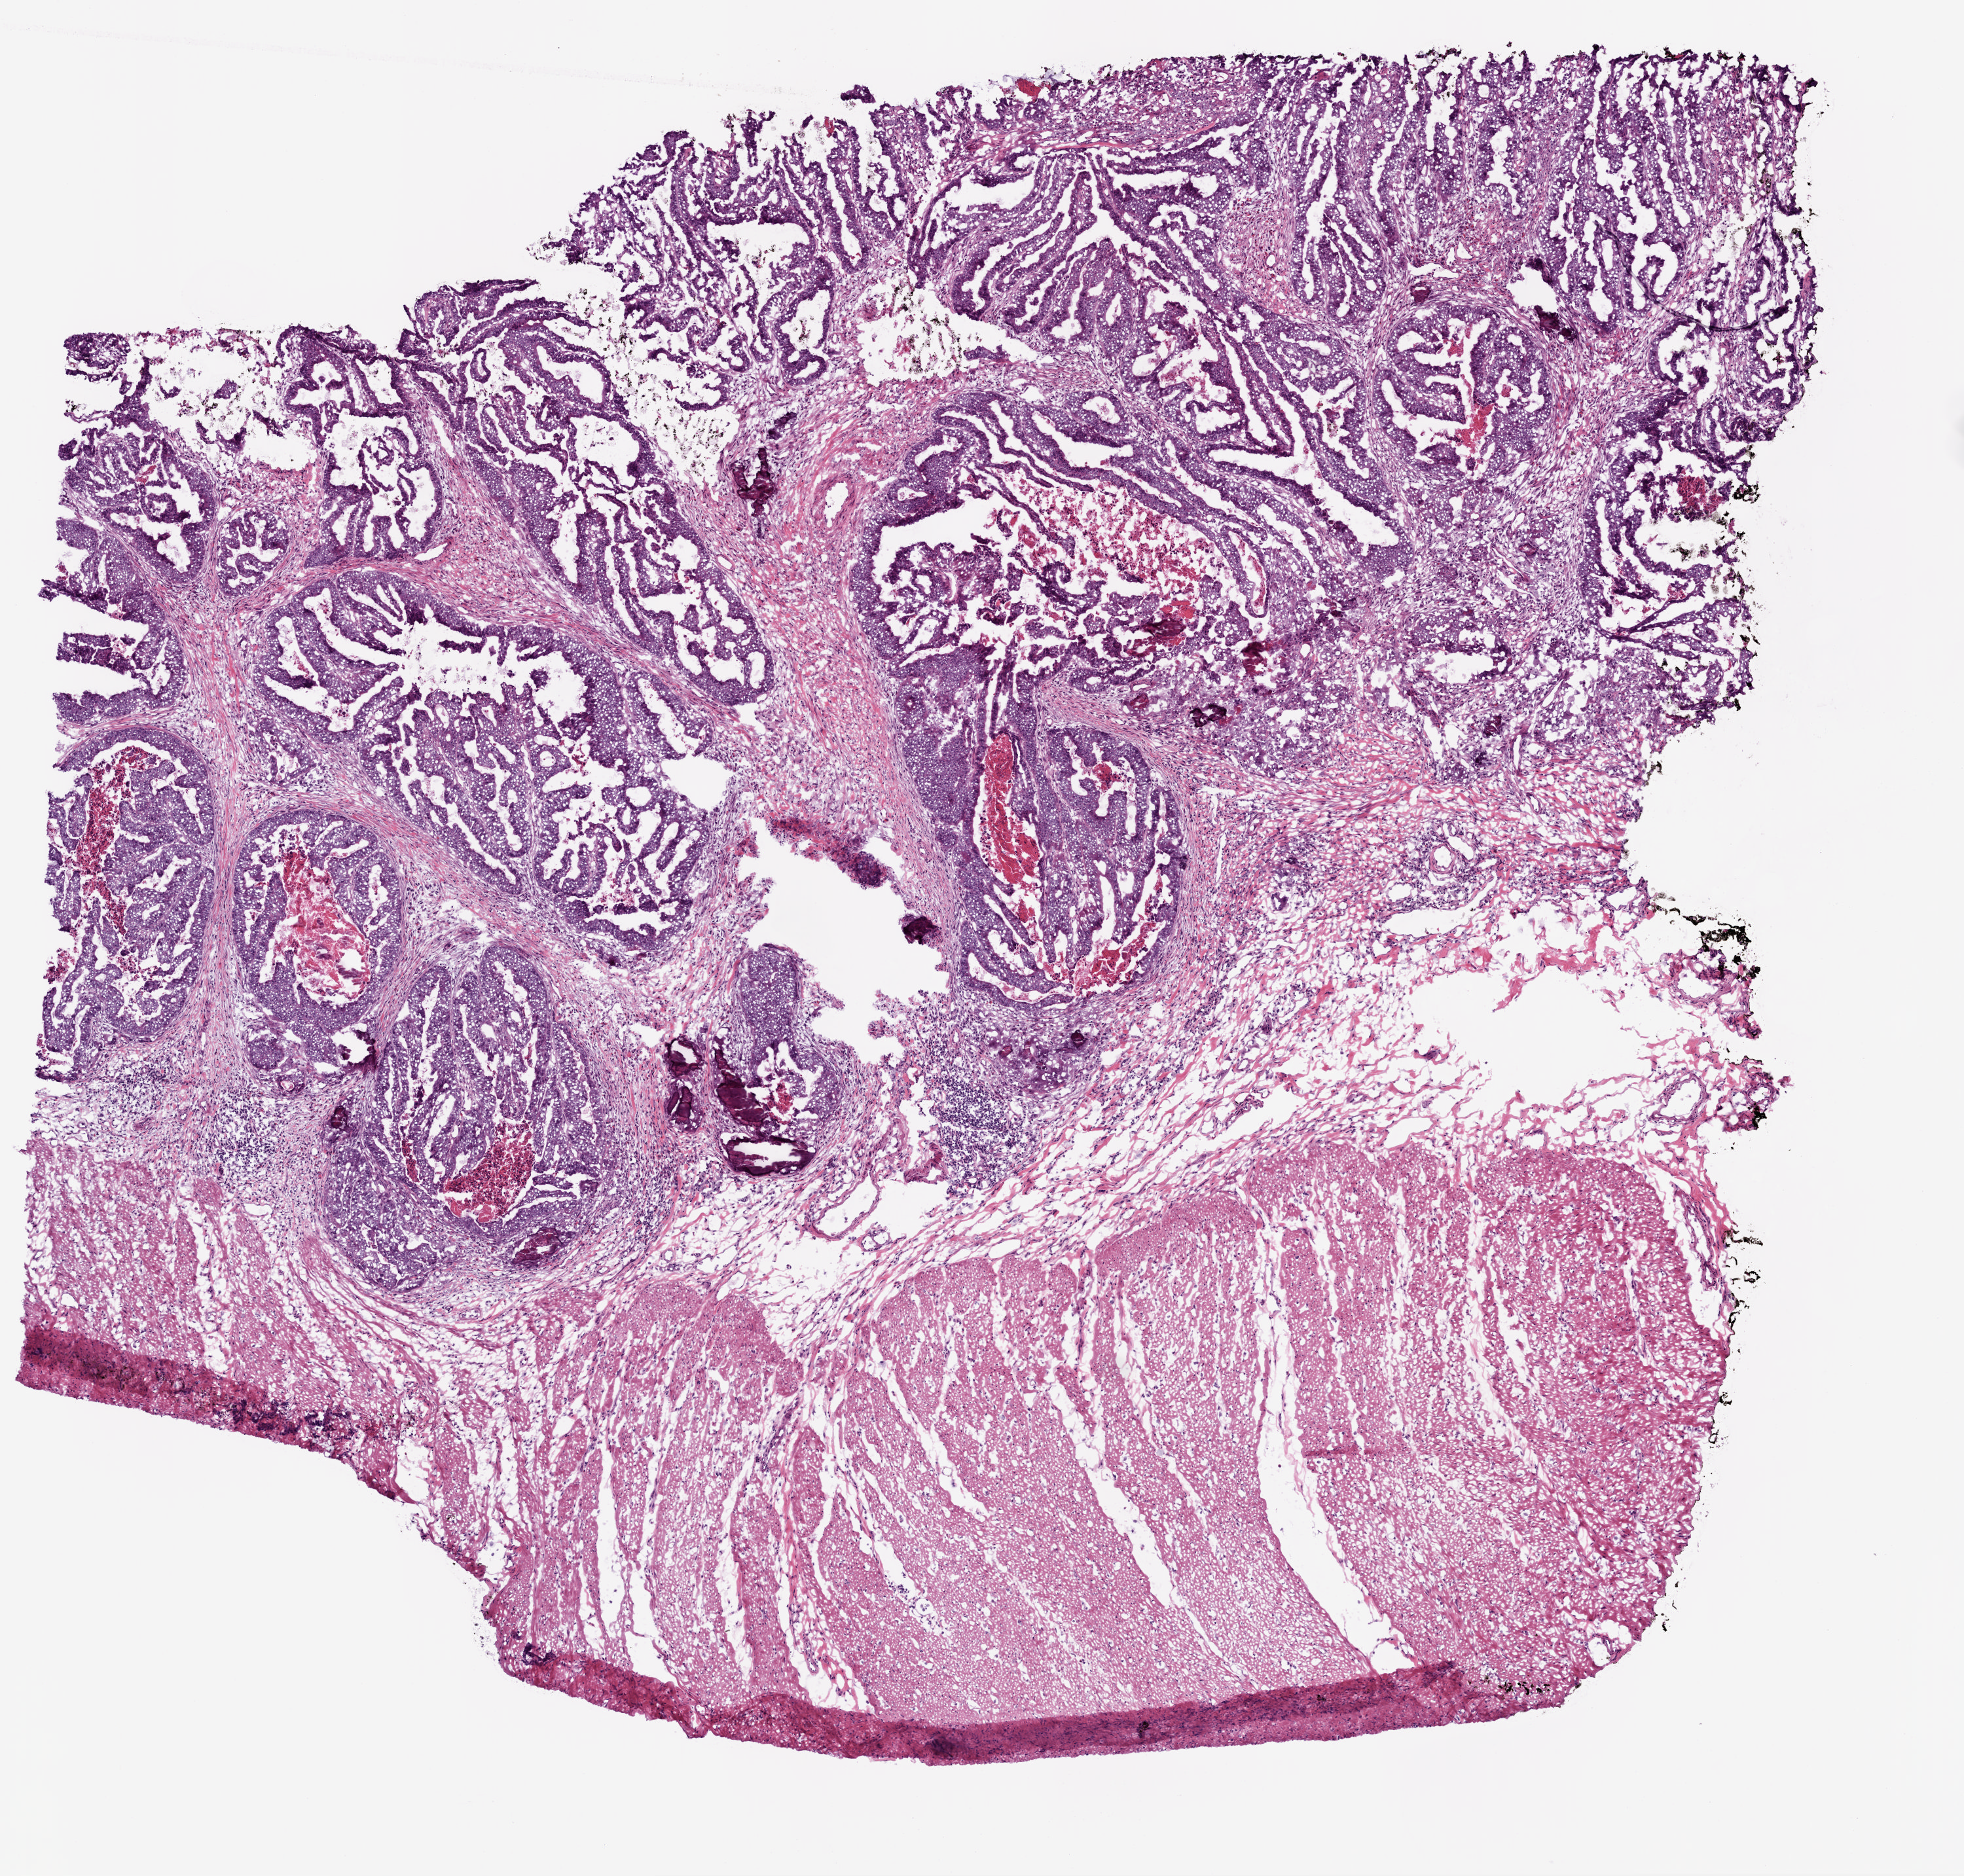
Digitized H&E tissue section (whole slide), shown as a low-resolution overview of the whole scanned area (about 6.0 x 5.7 mm). Frozen section. Colon, primary tumour sample. Male patient; age at initial diagnosis 74 years. Slide review estimates, as recorded: tumour cells 60%, tumour nuclei 70%, normal cells 30%, stromal cells 5%, necrosis 5%. Infiltration values recorded for this section: lymphocyte infiltration 15%, monocyte infiltration 1%, neutrophil infiltration 5%.
Pathologic diagnosis: Adenocarcinoma, NOS (sigmoid colon). AJCC pathologic stage: I.